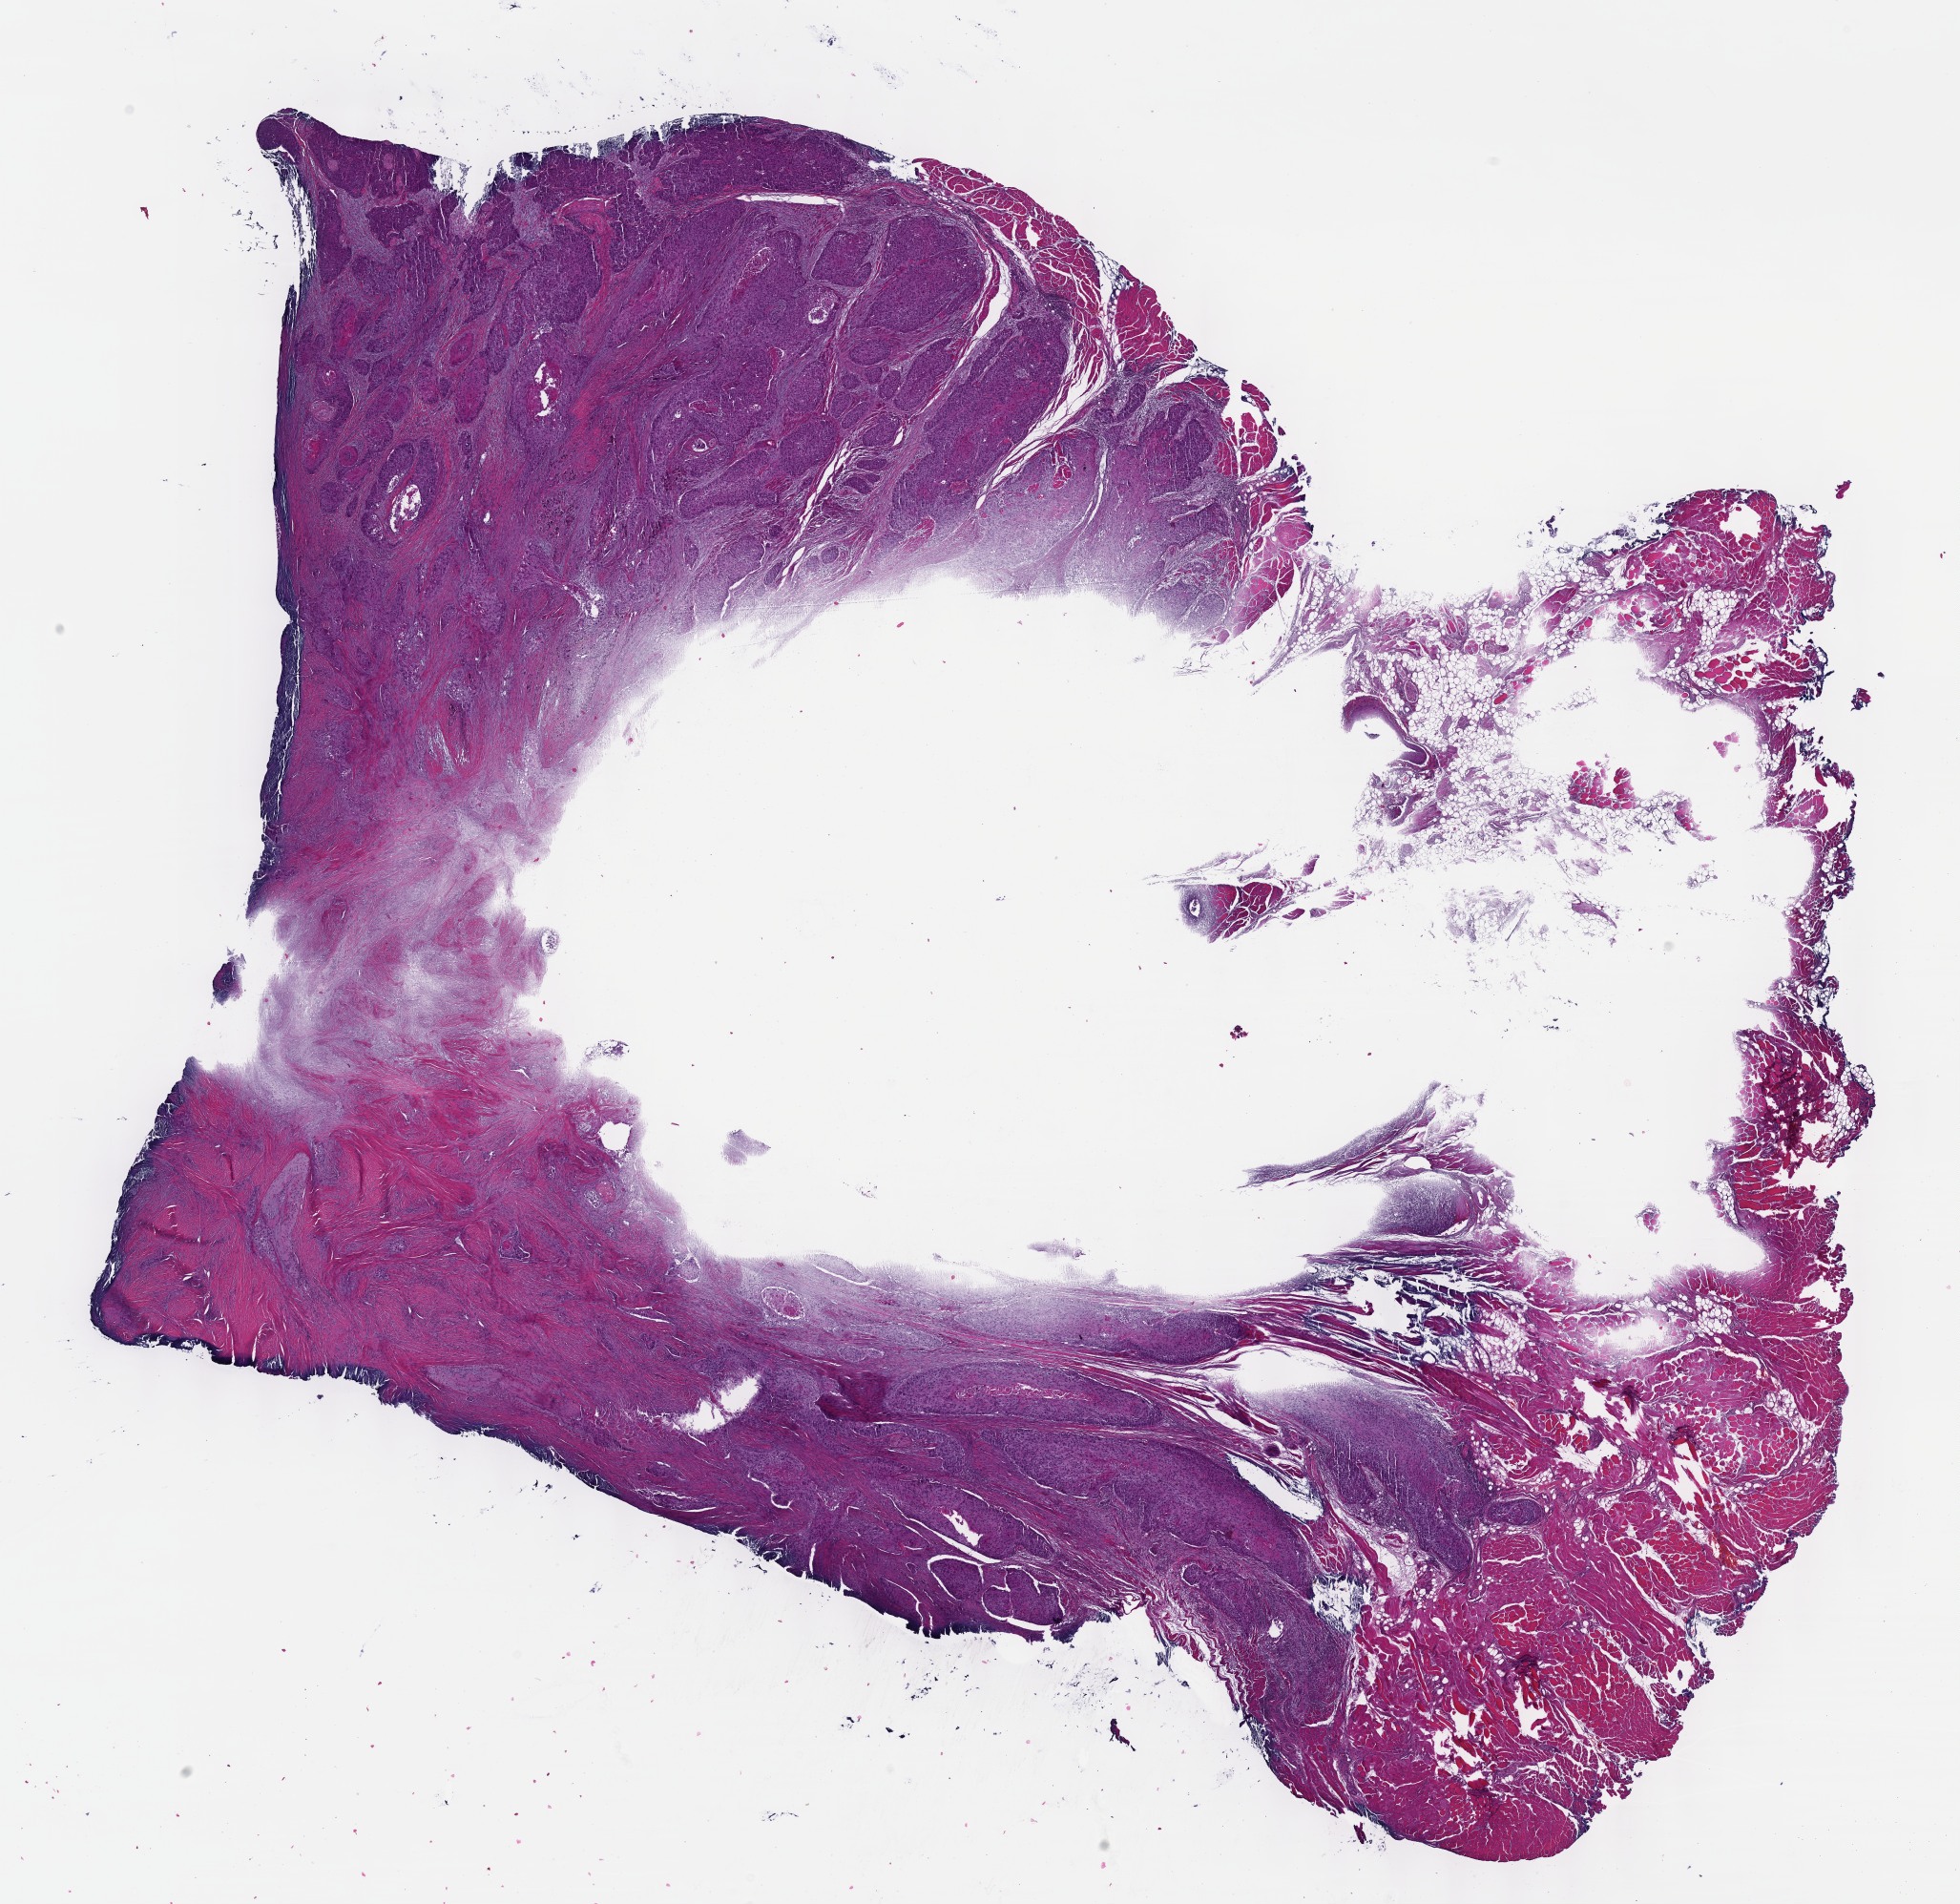
Digitized H&E-stained tissue section (whole slide), a low-resolution overview of the entire scanned area, about 16.6 x 16.1 mm (from a 40x scan); formalin-fixed paraffin-embedded (FFPE) diagnostic section; head and neck, primary tumour sample. Female patient; age at initial diagnosis 67 years. Histologic grade: G2 (moderately differentiated).
Laterality: right. AJCC pathologic stage: II. TNM: T2 NX. Pathologic diagnosis: Squamous cell carcinoma, NOS (floor of mouth, NOS).